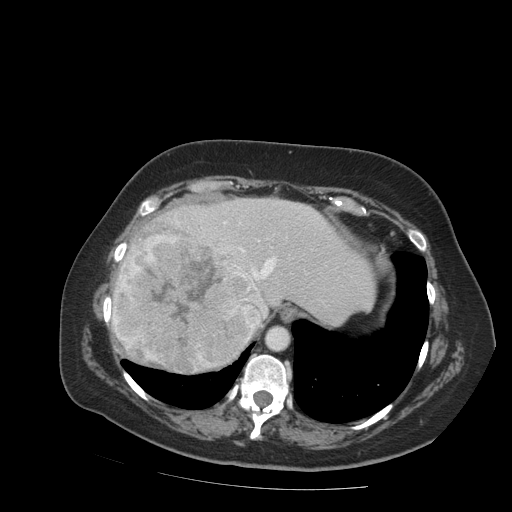
Contrast-enhanced abdominal CT (liver protocol), one axial slice. Slice 71 of 99 in the series (ordered by position). Soft-tissue window (W 400 / L 40 HU). 512 × 512 image matrix, field of view 400 × 400 mm. Case-level facts recorded for this patient, not image findings: diagnosis: hepatocellular carcinoma (patient treated with transarterial chemoembolisation; whether this scan precedes or follows treatment is not stated here); TNM stage (as recorded): Stage-IVB; Child-Pugh class: A; tumour differentiation: moderately differentiated; tumour nodularity: uninodular.
Annotated regions visible in this slice (semi-automatic segmentation, software-assisted and operator-edited):
- abdominal aorta: bounding box <267,327,289,350> (left, top, right, bottom; pixels)
- liver parenchyma outside the tumour (the mass and vessels are separate outlines, so this box may not span the whole liver): <112,198,376,370>
- mass: <110,227,266,374>
- liver vessels: <177,221,277,328>